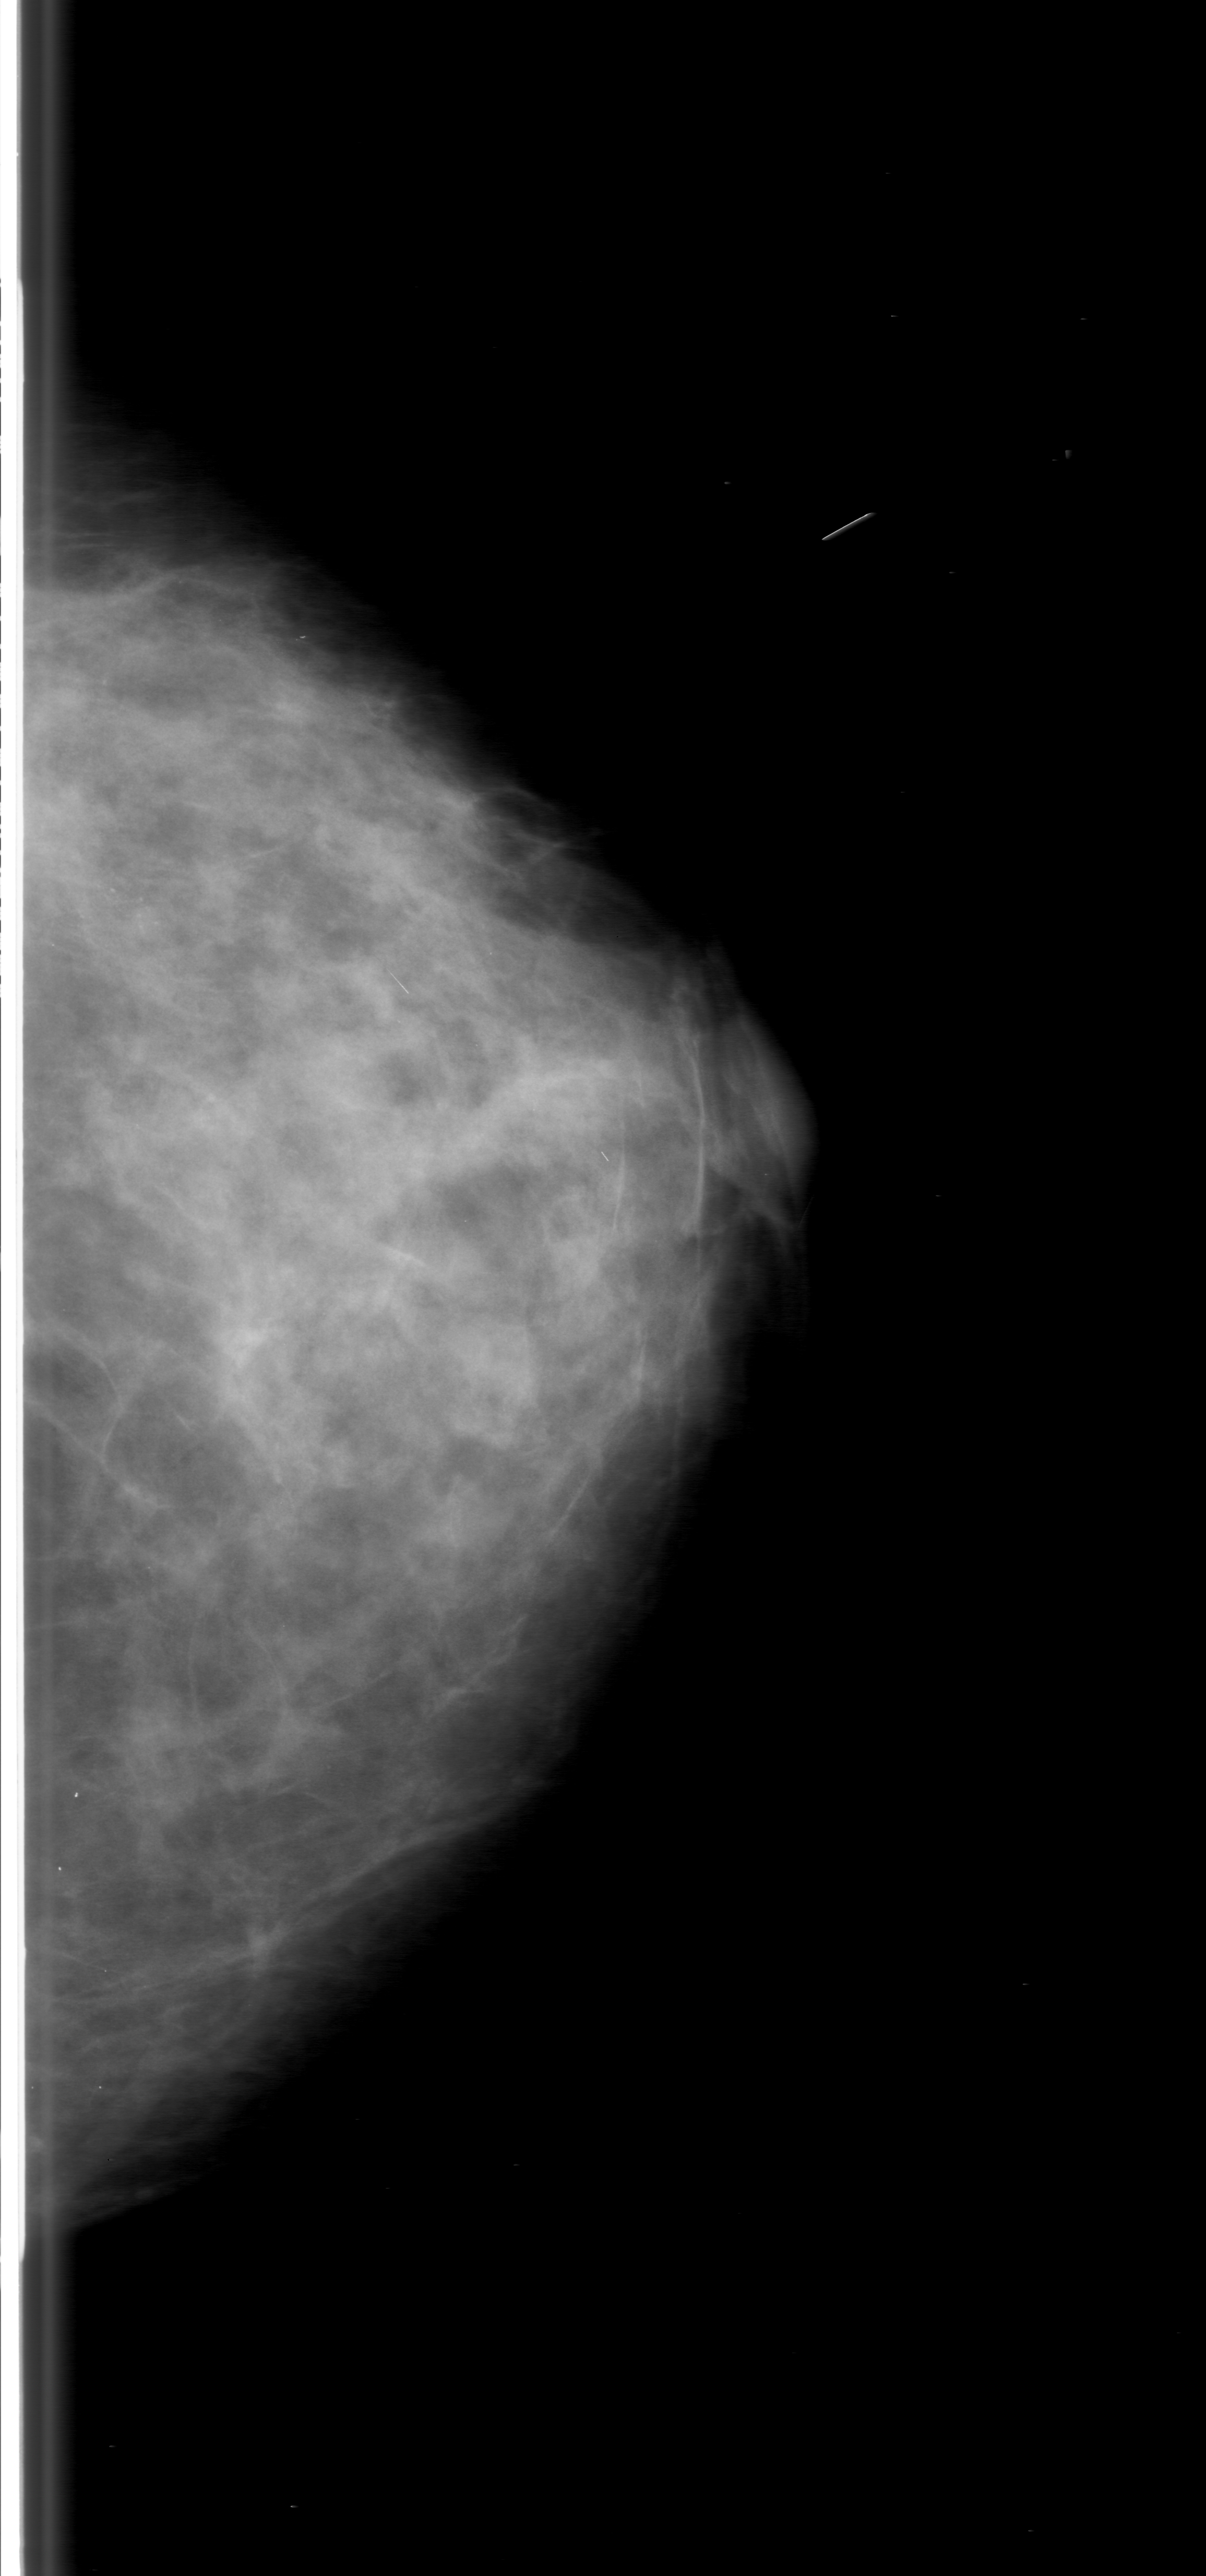
Digitized screen-film mammogram. Left breast. CC view. Breast composition: heterogeneously dense (BI-RADS density category 3 of 4). 1206 × 2576 image matrix.
Expert-marked regions of interest on this film, with their recorded descriptors:
- calcifications, morphology amorphous, distribution clustered; BI-RADS assessment category 3; subtlety rating 2 on a 1 (subtle) to 5 (obvious) scale; pathology result (as recorded, not read from the image): malignant: box from (x=34, y=719) to (x=303, y=1109) px